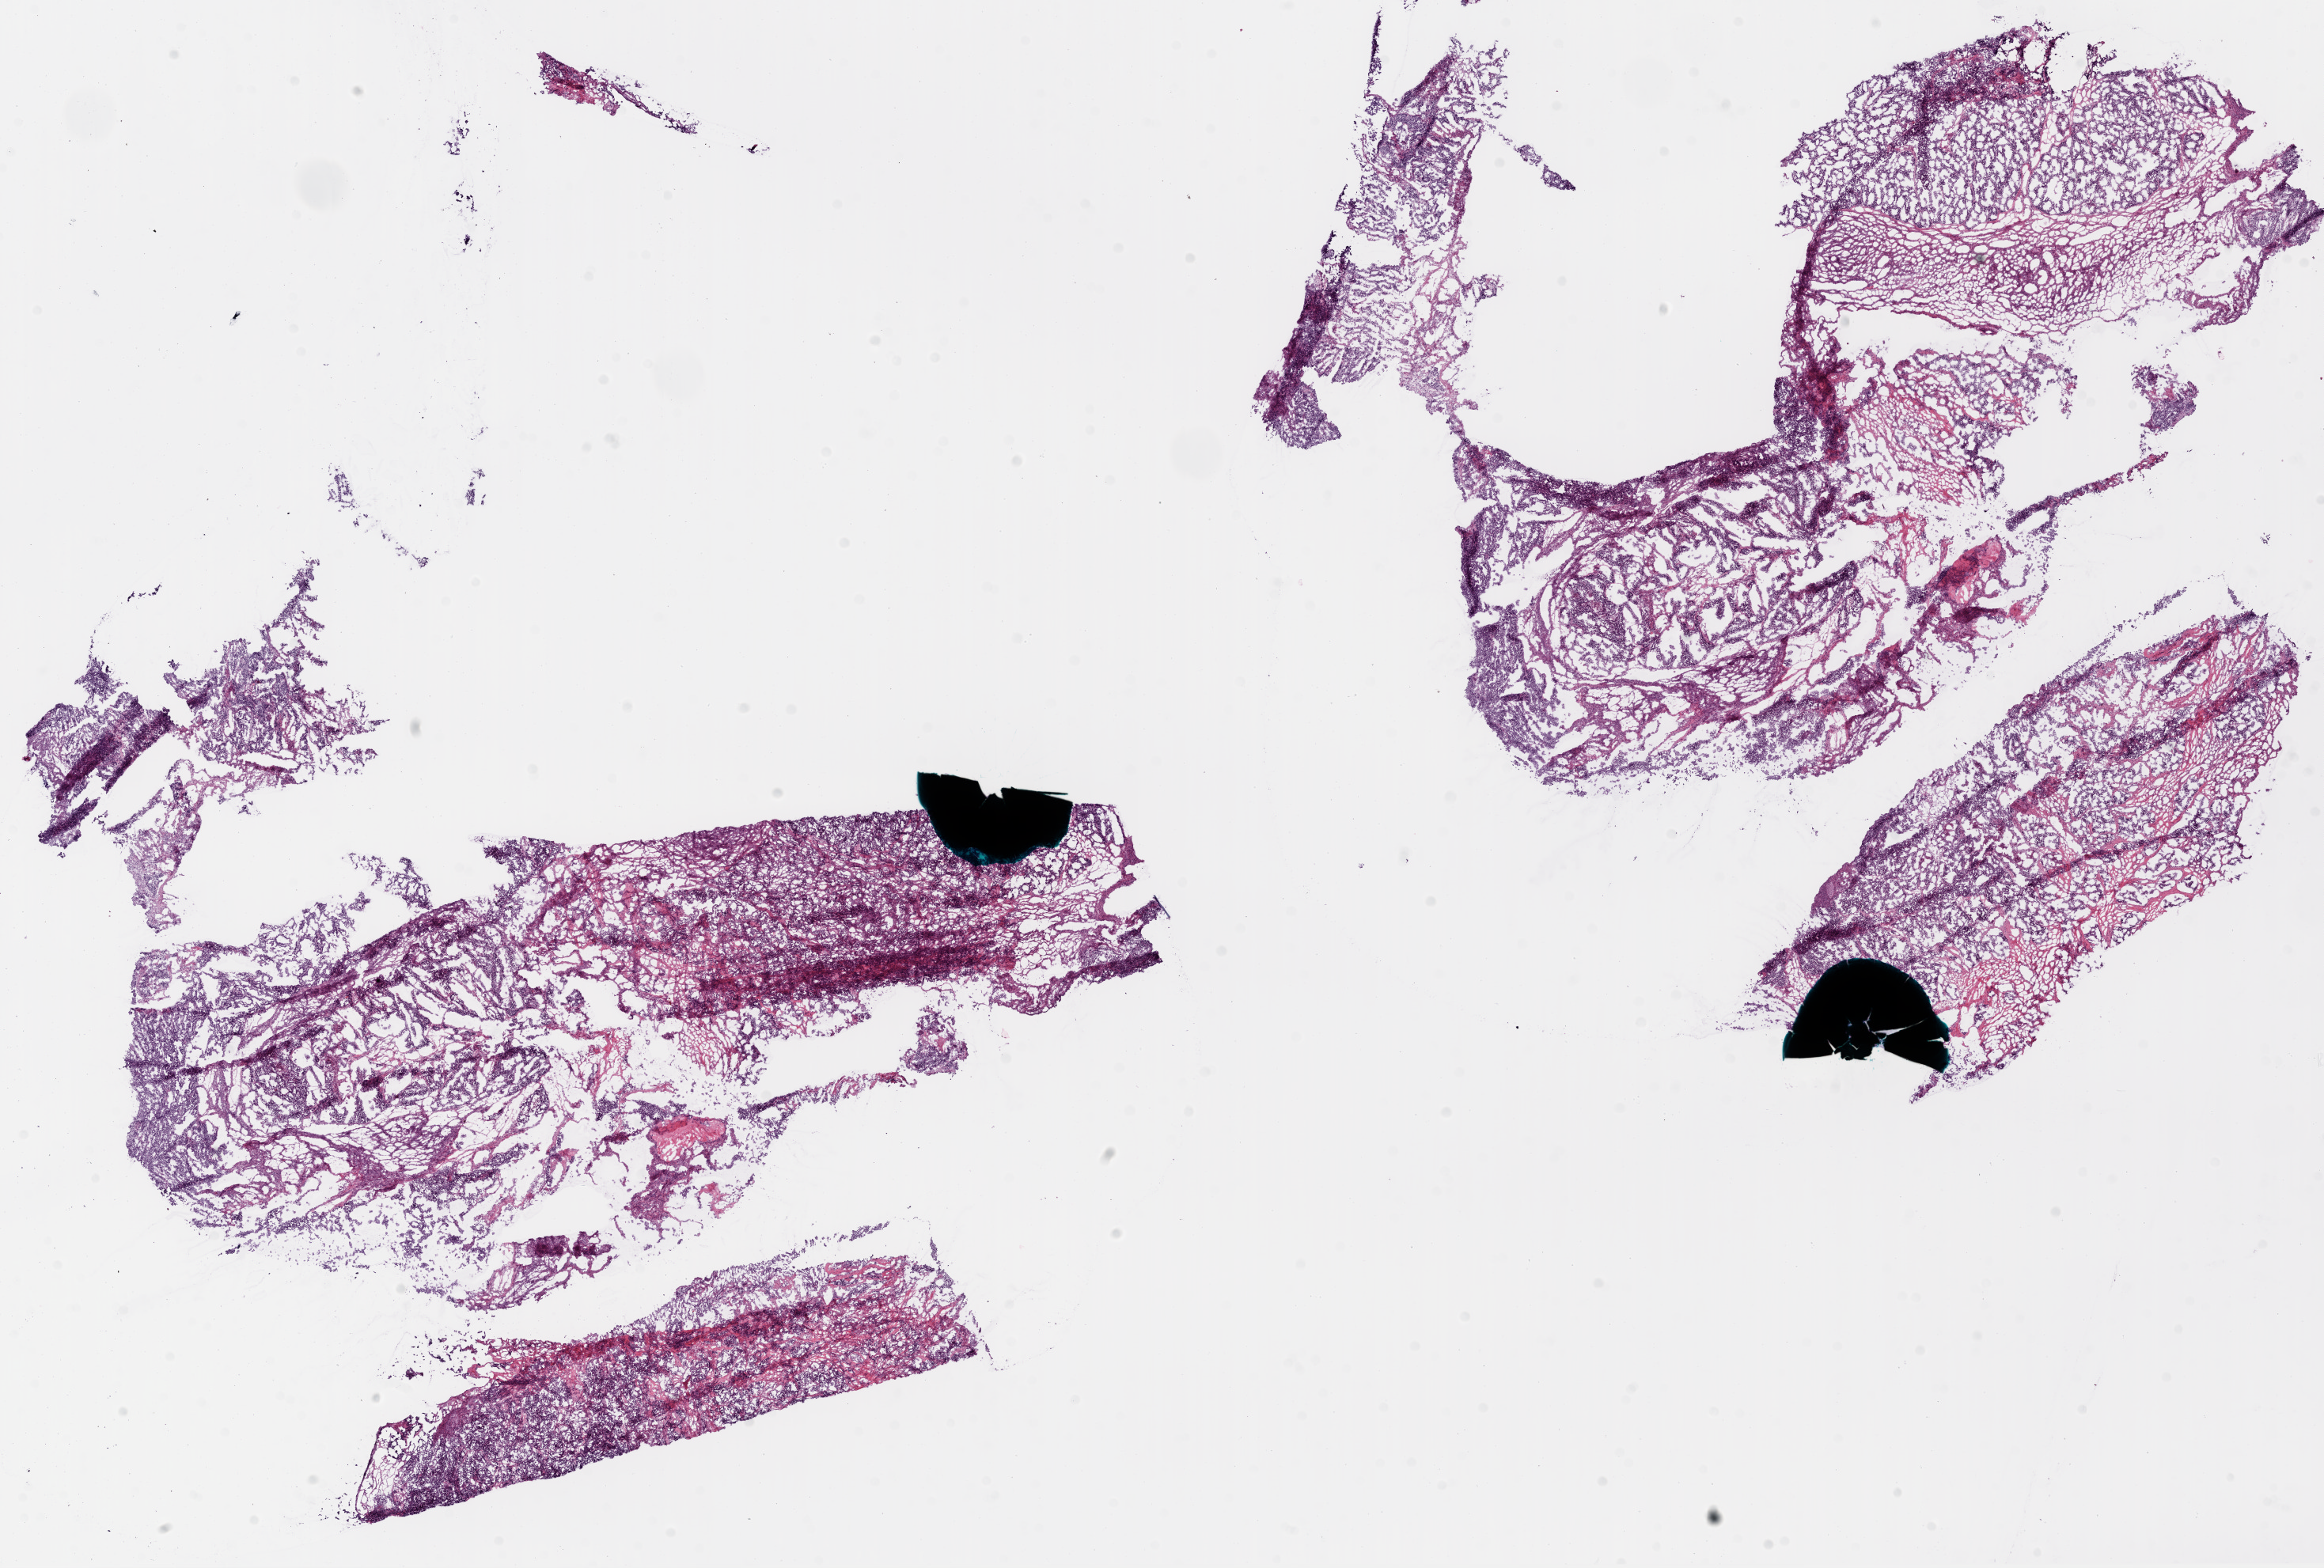
H&E whole-slide image, whole scanned area (about 23.7 x 16.0 mm, slide scanned at 20x) shown as a low-resolution overview. Frozen section. Primary tumour sample from the ovary. Female, age 60 years at initial diagnosis. Histologic grade: G2 (moderately differentiated). Composition of this section per pathologist review: tumour cells 62%, tumour nuclei 90%, normal cells 0%, stromal cells 20%, necrosis 18%.
FIGO stage: IB. Histologic diagnosis: Serous cystadenocarcinoma, NOS.